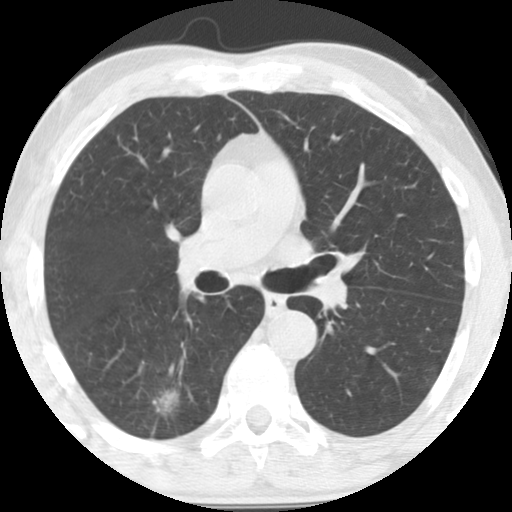
Chest CT (low-dose screening protocol), one axial image. Baseline annual screen. Lung window (W 1500 / L -600 HU). Slice 52 of 135 in the series. Male, age 64 years at enrolment.
Lesion marked by an expert reader, bounding box <115,365,189,432> (left, top, right, bottom; pixels). The exam's reader record, not a measurement of the box and not confirmed to be the same lesion: non-calcified nodule or mass ≥4 mm, right lower lobe, 36 × 26 mm, spiculated (stellate) margins, soft tissue attenuation. Participant outcome: lung cancer diagnosed 20 days after this screen — adenocarcinoma, NOS, right lower lobe, moderately differentiated (G2), stage IA (AJCC 6th edition), 28 mm at pathology.